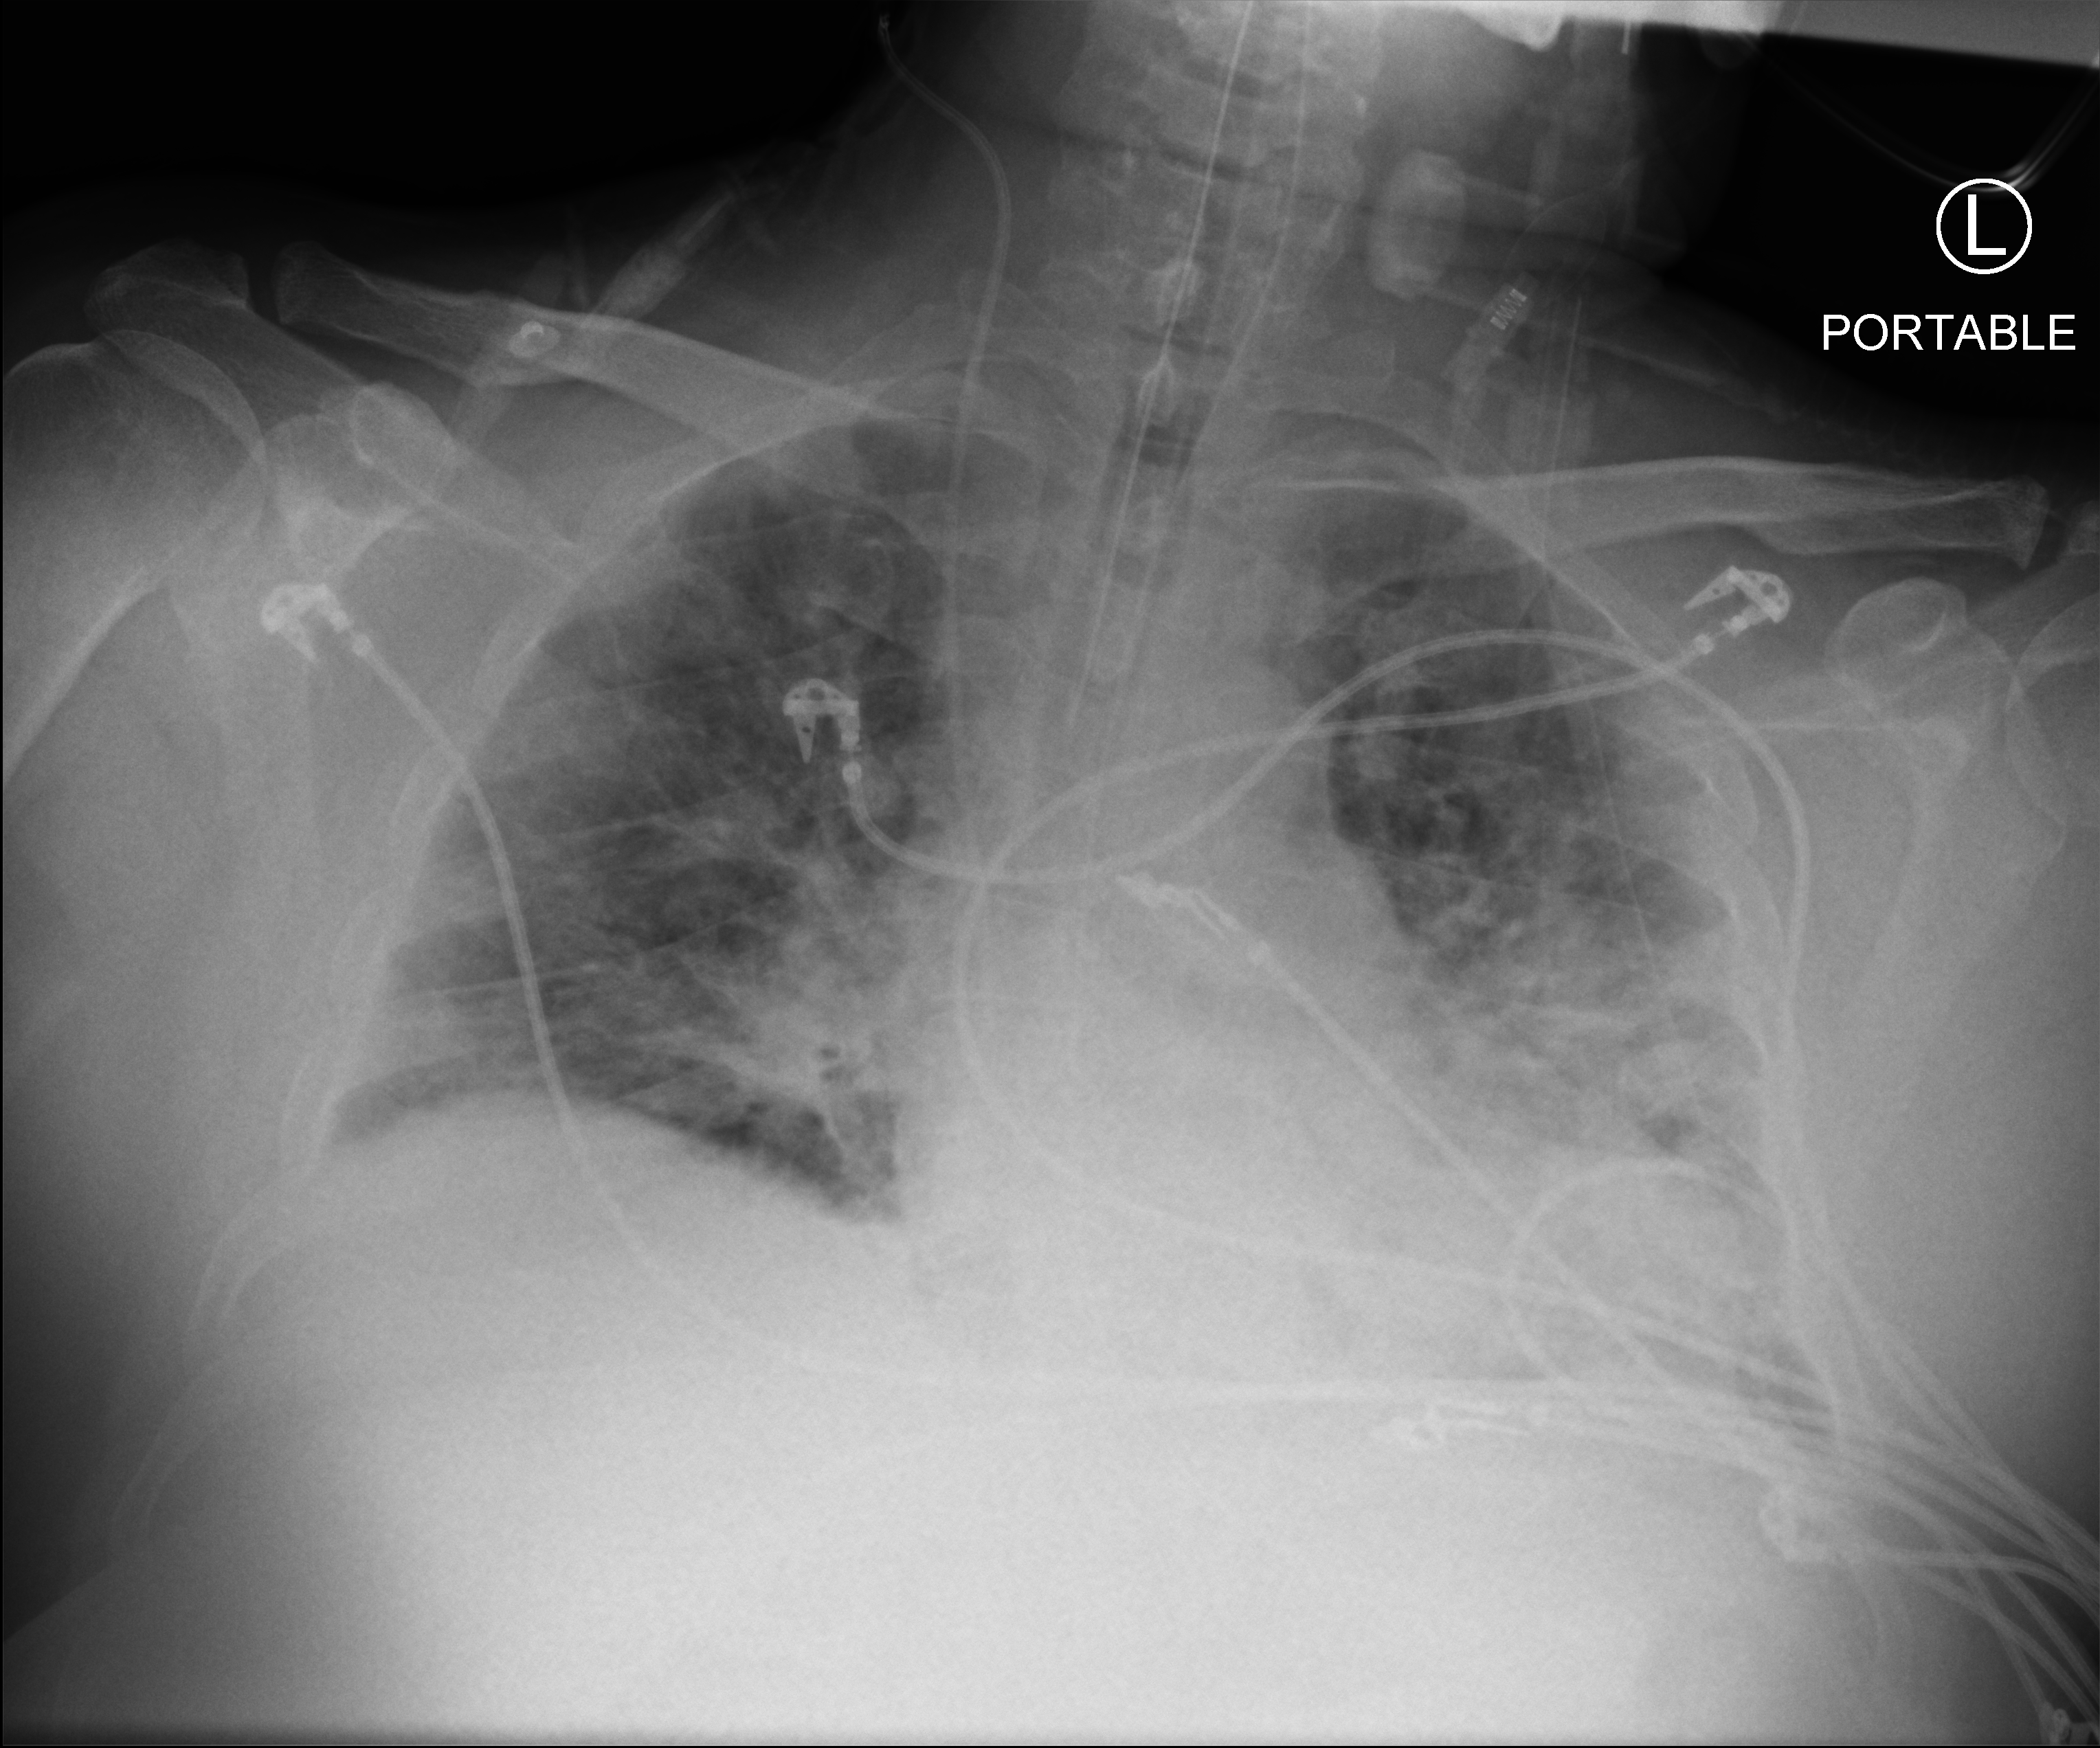
Bedside chest radiograph (computed radiography). Patient hospitalised with COVID-19; male, aged 18–59 years.
Admission-level facts for this patient (not findings on this image; timing relative to this image not recorded):
- diabetes (admission record): yes